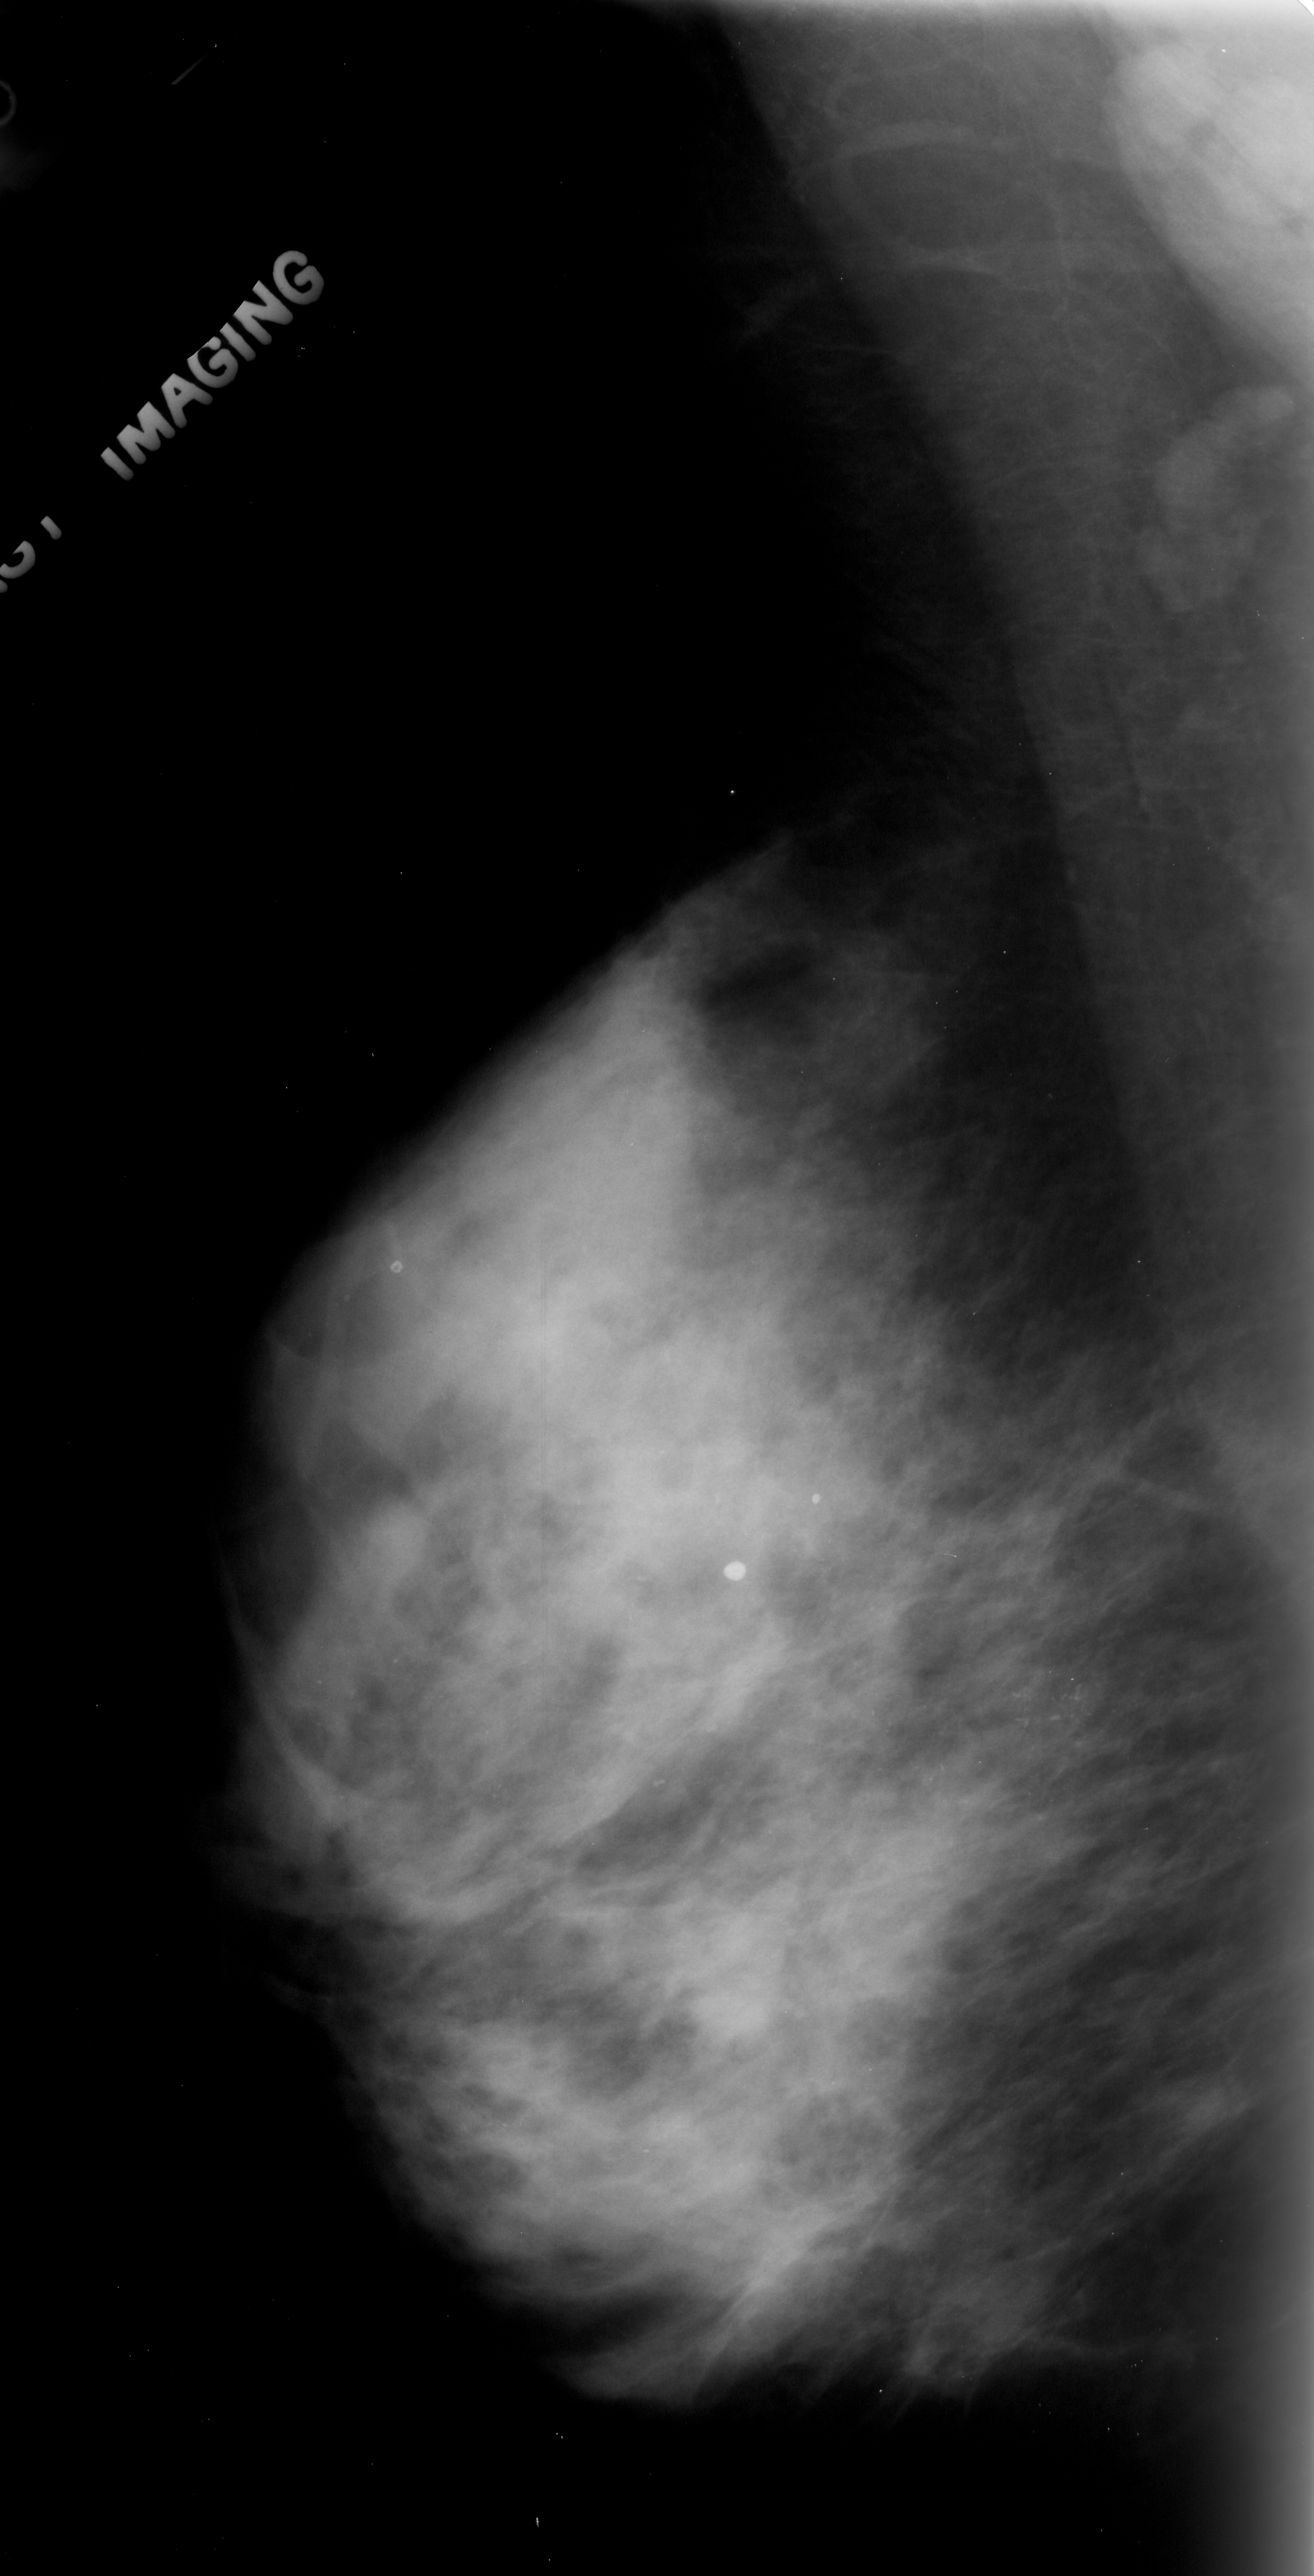
Scanned film-screen mammogram; left breast; MLO view; BI-RADS breast density category 4 (scale 1–4); 1314 × 2576 image matrix.
Expert-marked regions of interest on this film, with their recorded descriptors:
- calcifications, morphology pleomorphic, distribution linear; BI-RADS assessment category 4; pathology (as recorded): malignant: box from (x=891, y=1659) to (x=1146, y=1811) px